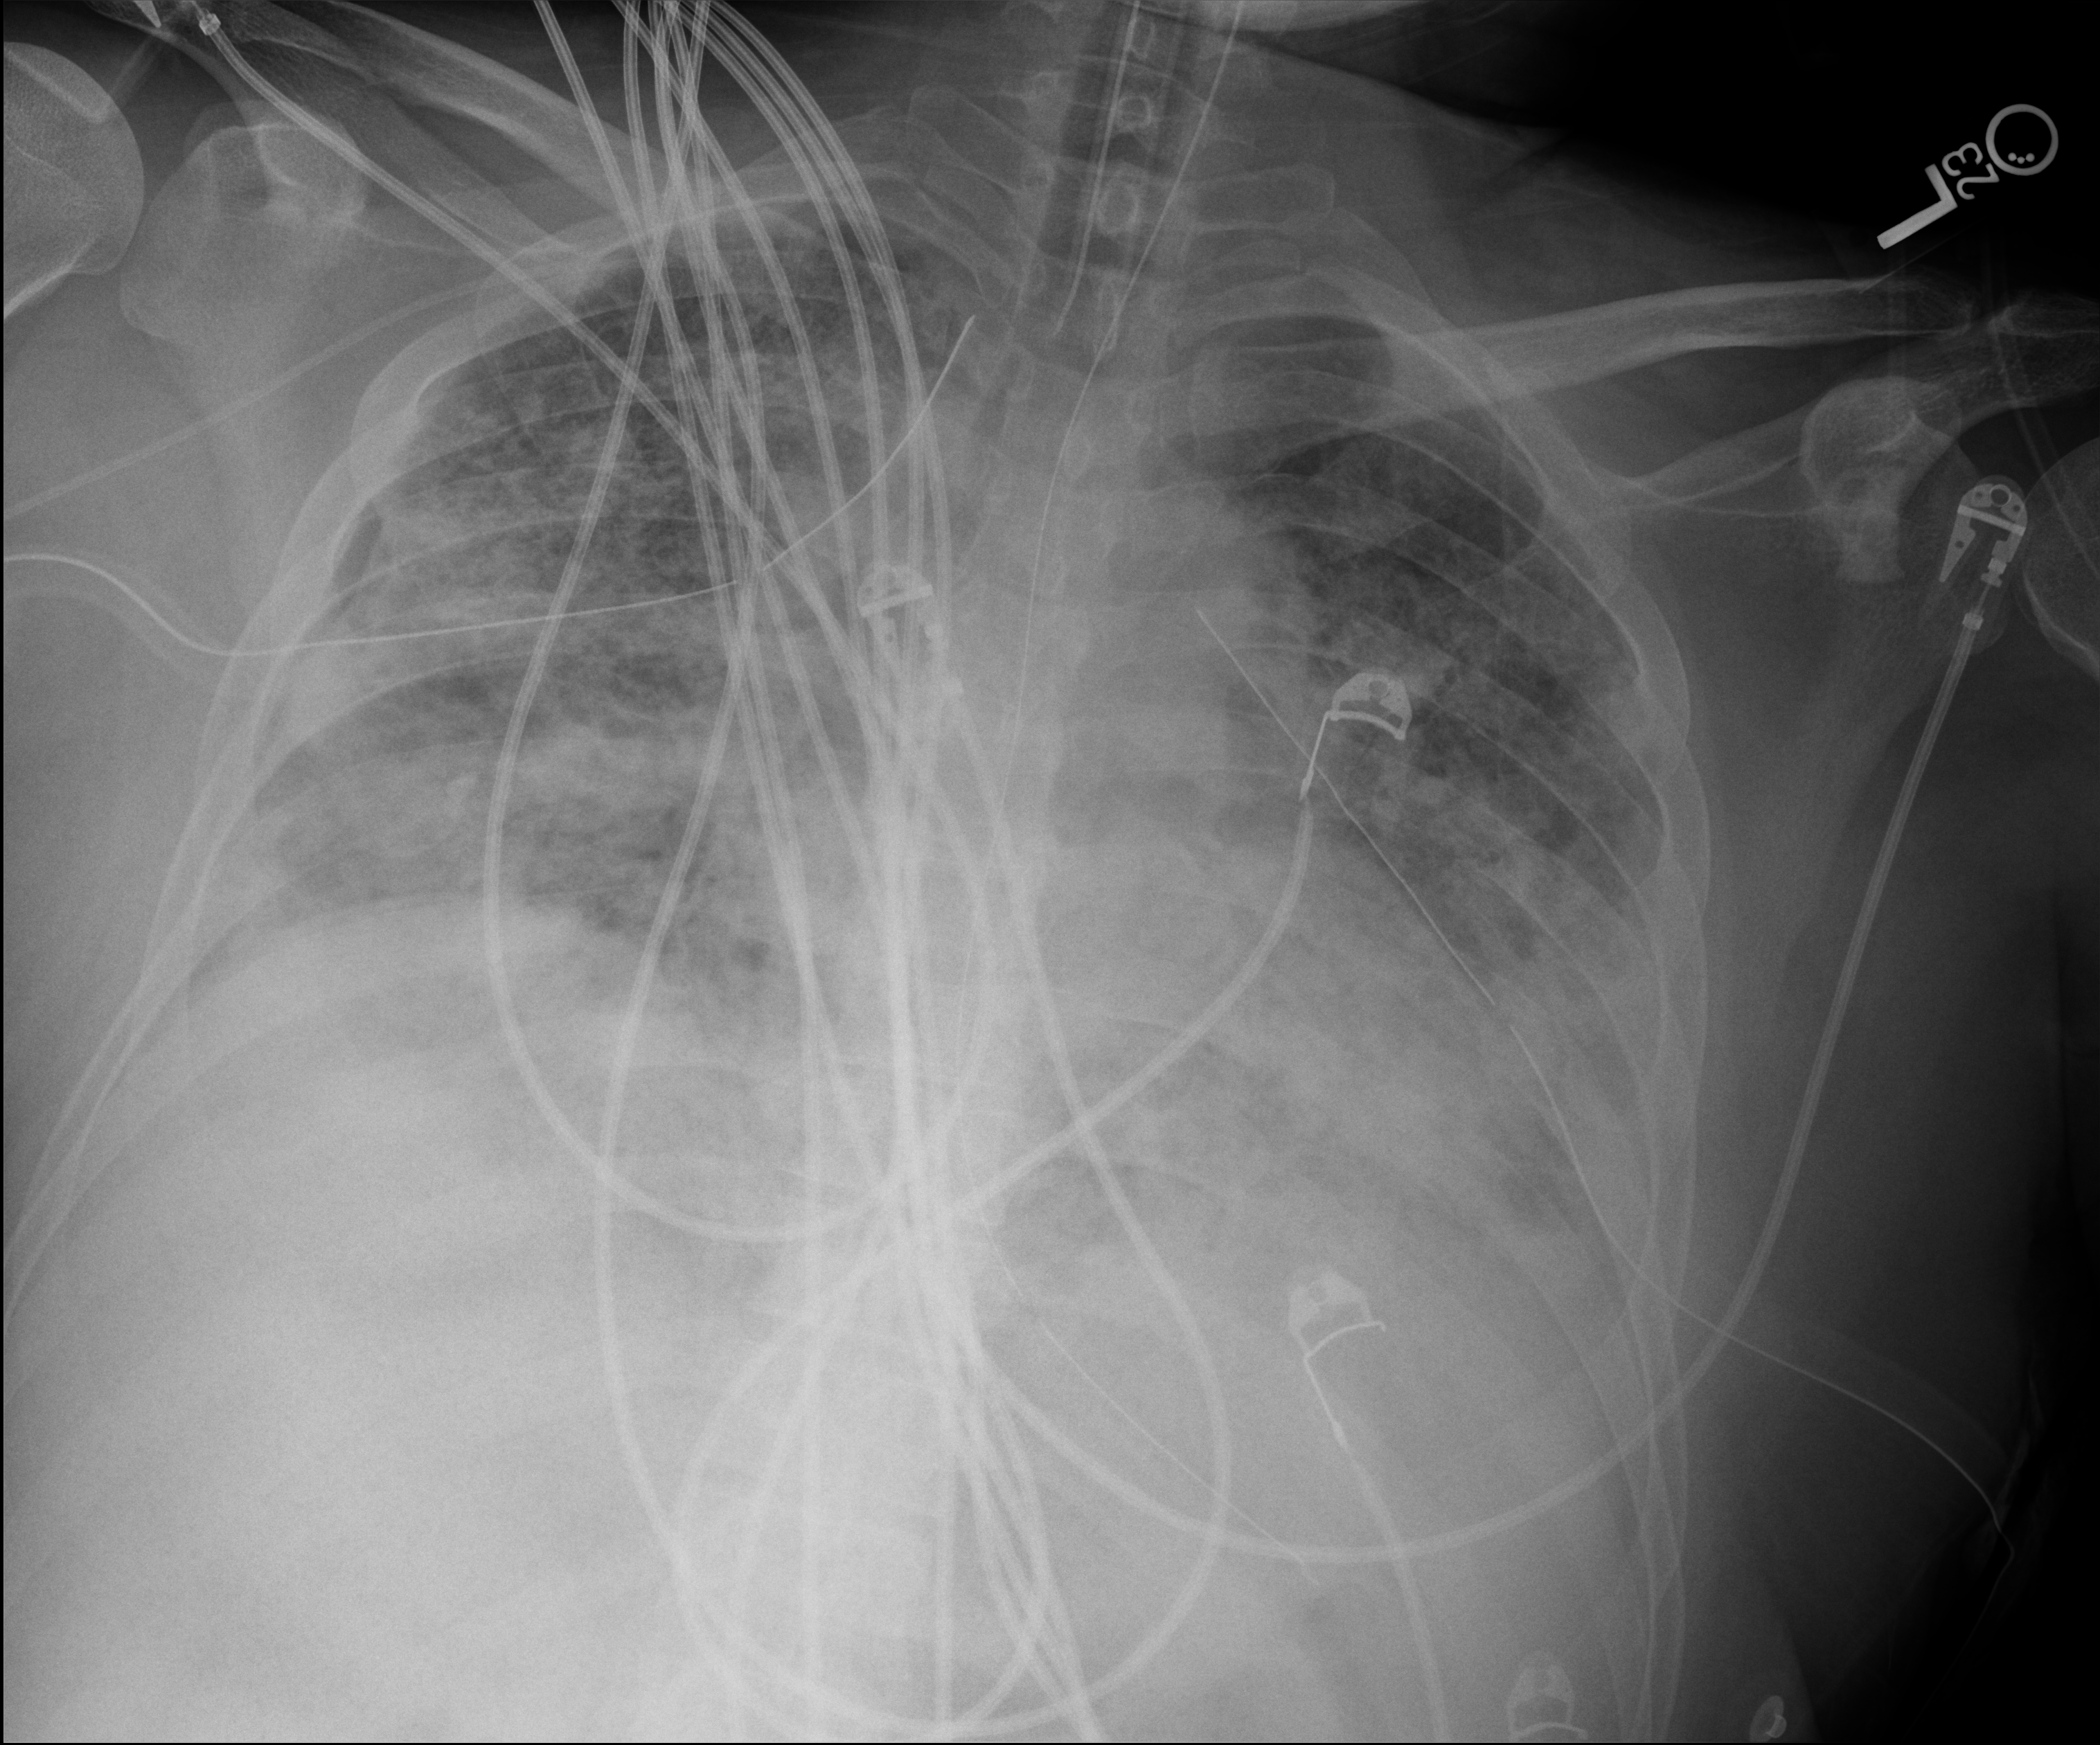
Chest X-ray (portable); anteroposterior (AP) projection. Male patient hospitalised with COVID-19, age 18–59 years.
From the hospital-stay record, not from the radiograph (when in the stay this image was taken is not recorded):
- length of hospital stay: 63 days
- admitted to intensive care during this hospital stay: yes
- hypertension (admission record): yes